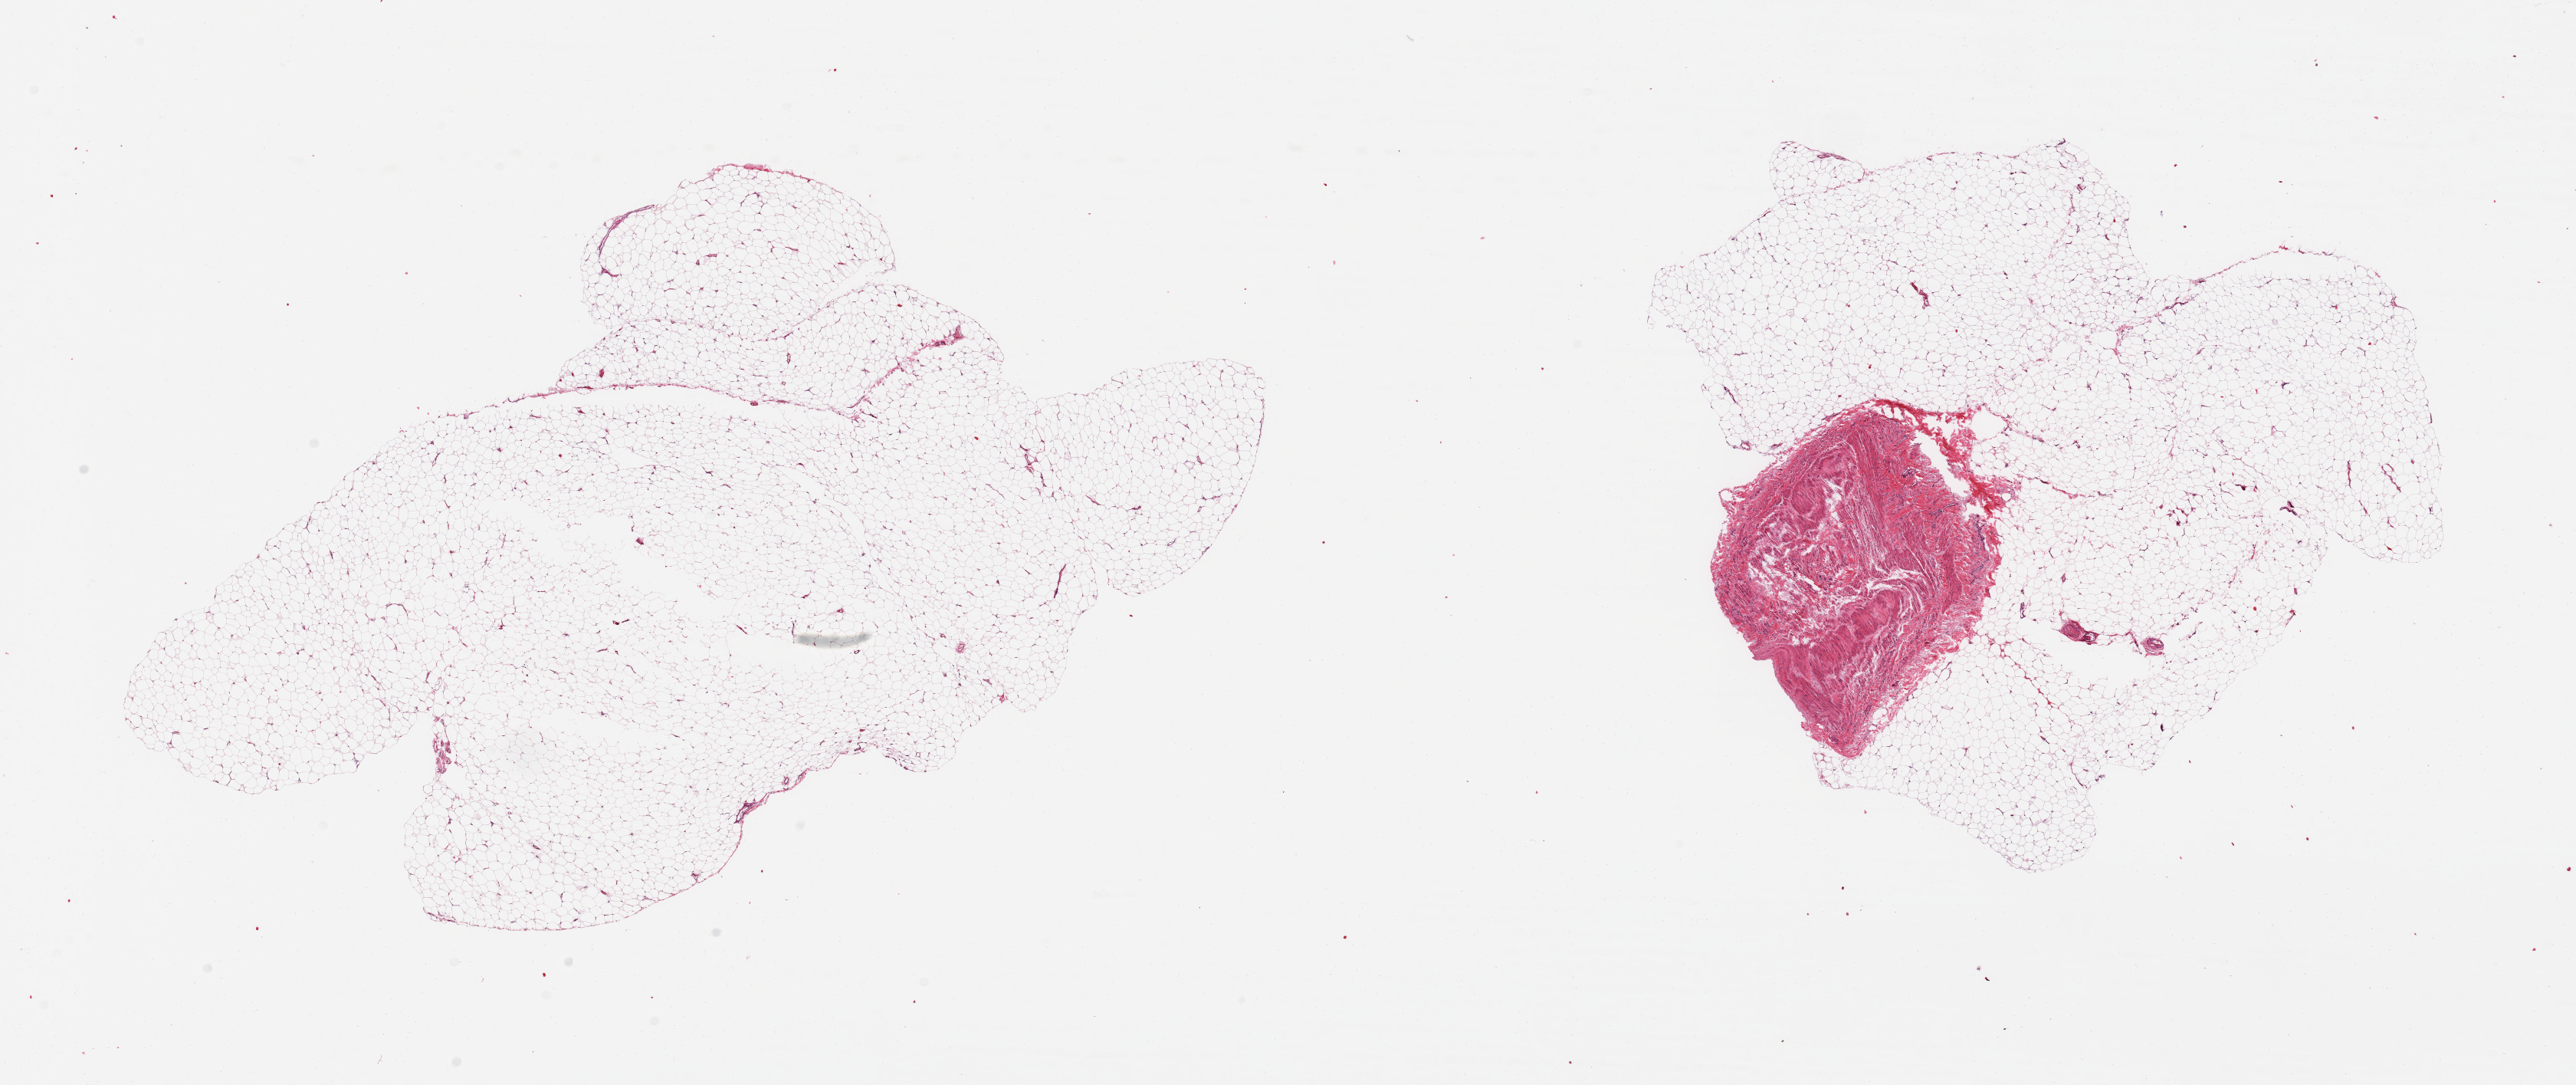
Whole-slide image, haematoxylin and eosin stain, brightfield, a low-resolution overview of the entire scanned area, about 26.6 x 11.2 mm. PAXgene-fixed, paraffin-embedded tissue. Target tissue: adipose tissue. Tissue donor sample.
Reviewer comment on this tissue sample: 2 pieces; 1 piece is ~20% fibrous/vascular.